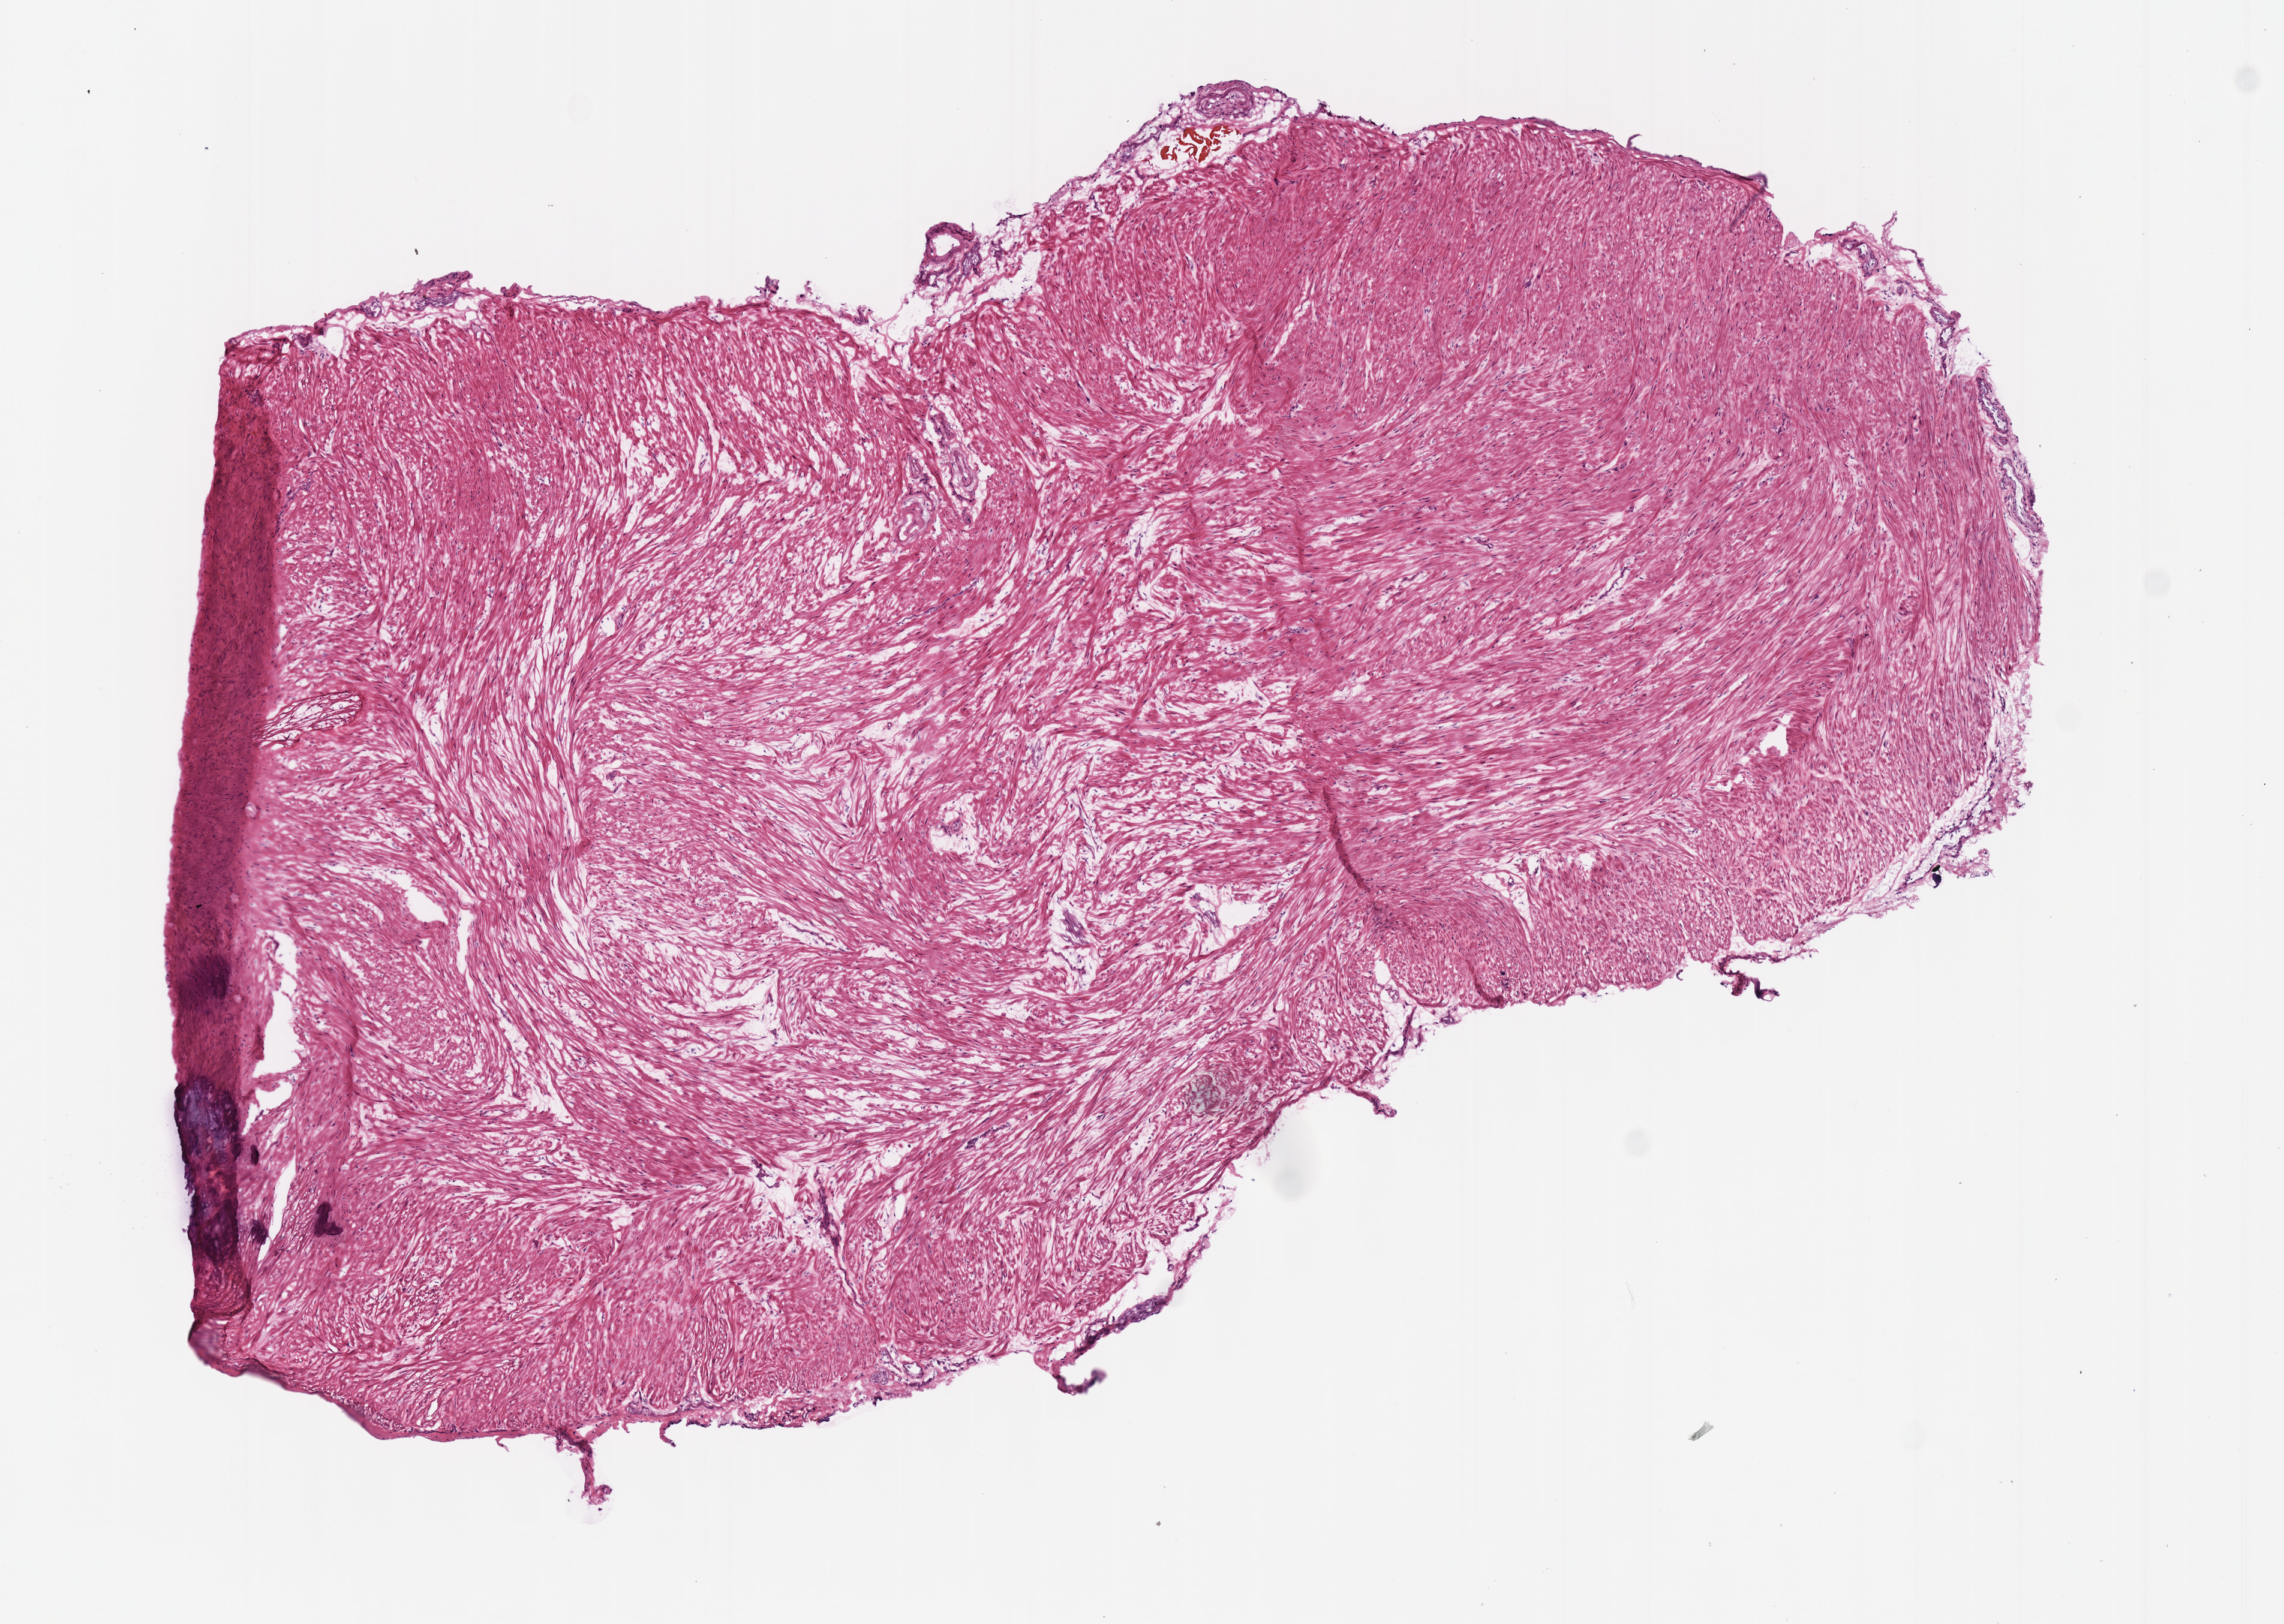
H&E whole-slide image, low-resolution overview of the scanned area, about 7.5 x 5.3 mm. Frozen section. Prostate, solid tissue normal (non-tumour tissue) sample. Patient: male, age at initial diagnosis 59 years.
• this section: solid tissue normal sample (biorepository sample class)
• patient diagnosis: Acinar cell carcinoma (prostate gland)